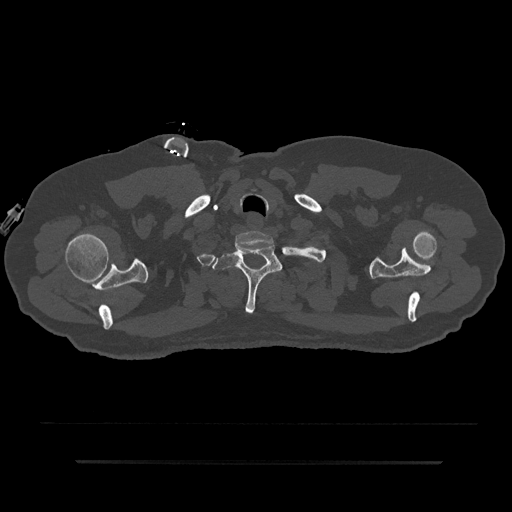
CT including the spine, one axial slice. Position 741 of 797 along the scan axis. 120 kVp. Bone window (W 1800 / L 400 HU). 512 × 512 image matrix, field of view 464 × 464 mm. Male patient, age 59 years. Case-level facts recorded for this patient, not image findings: primary cancer: bile ducts; vertebrae with lytic lesions (as recorded): T10.
Annotated regions visible in this slice (semi-automatic segmentation, software-assisted and operator-edited):
- T1 vertebra: bounding box <212,246,282,314> (left, top, right, bottom; pixels)